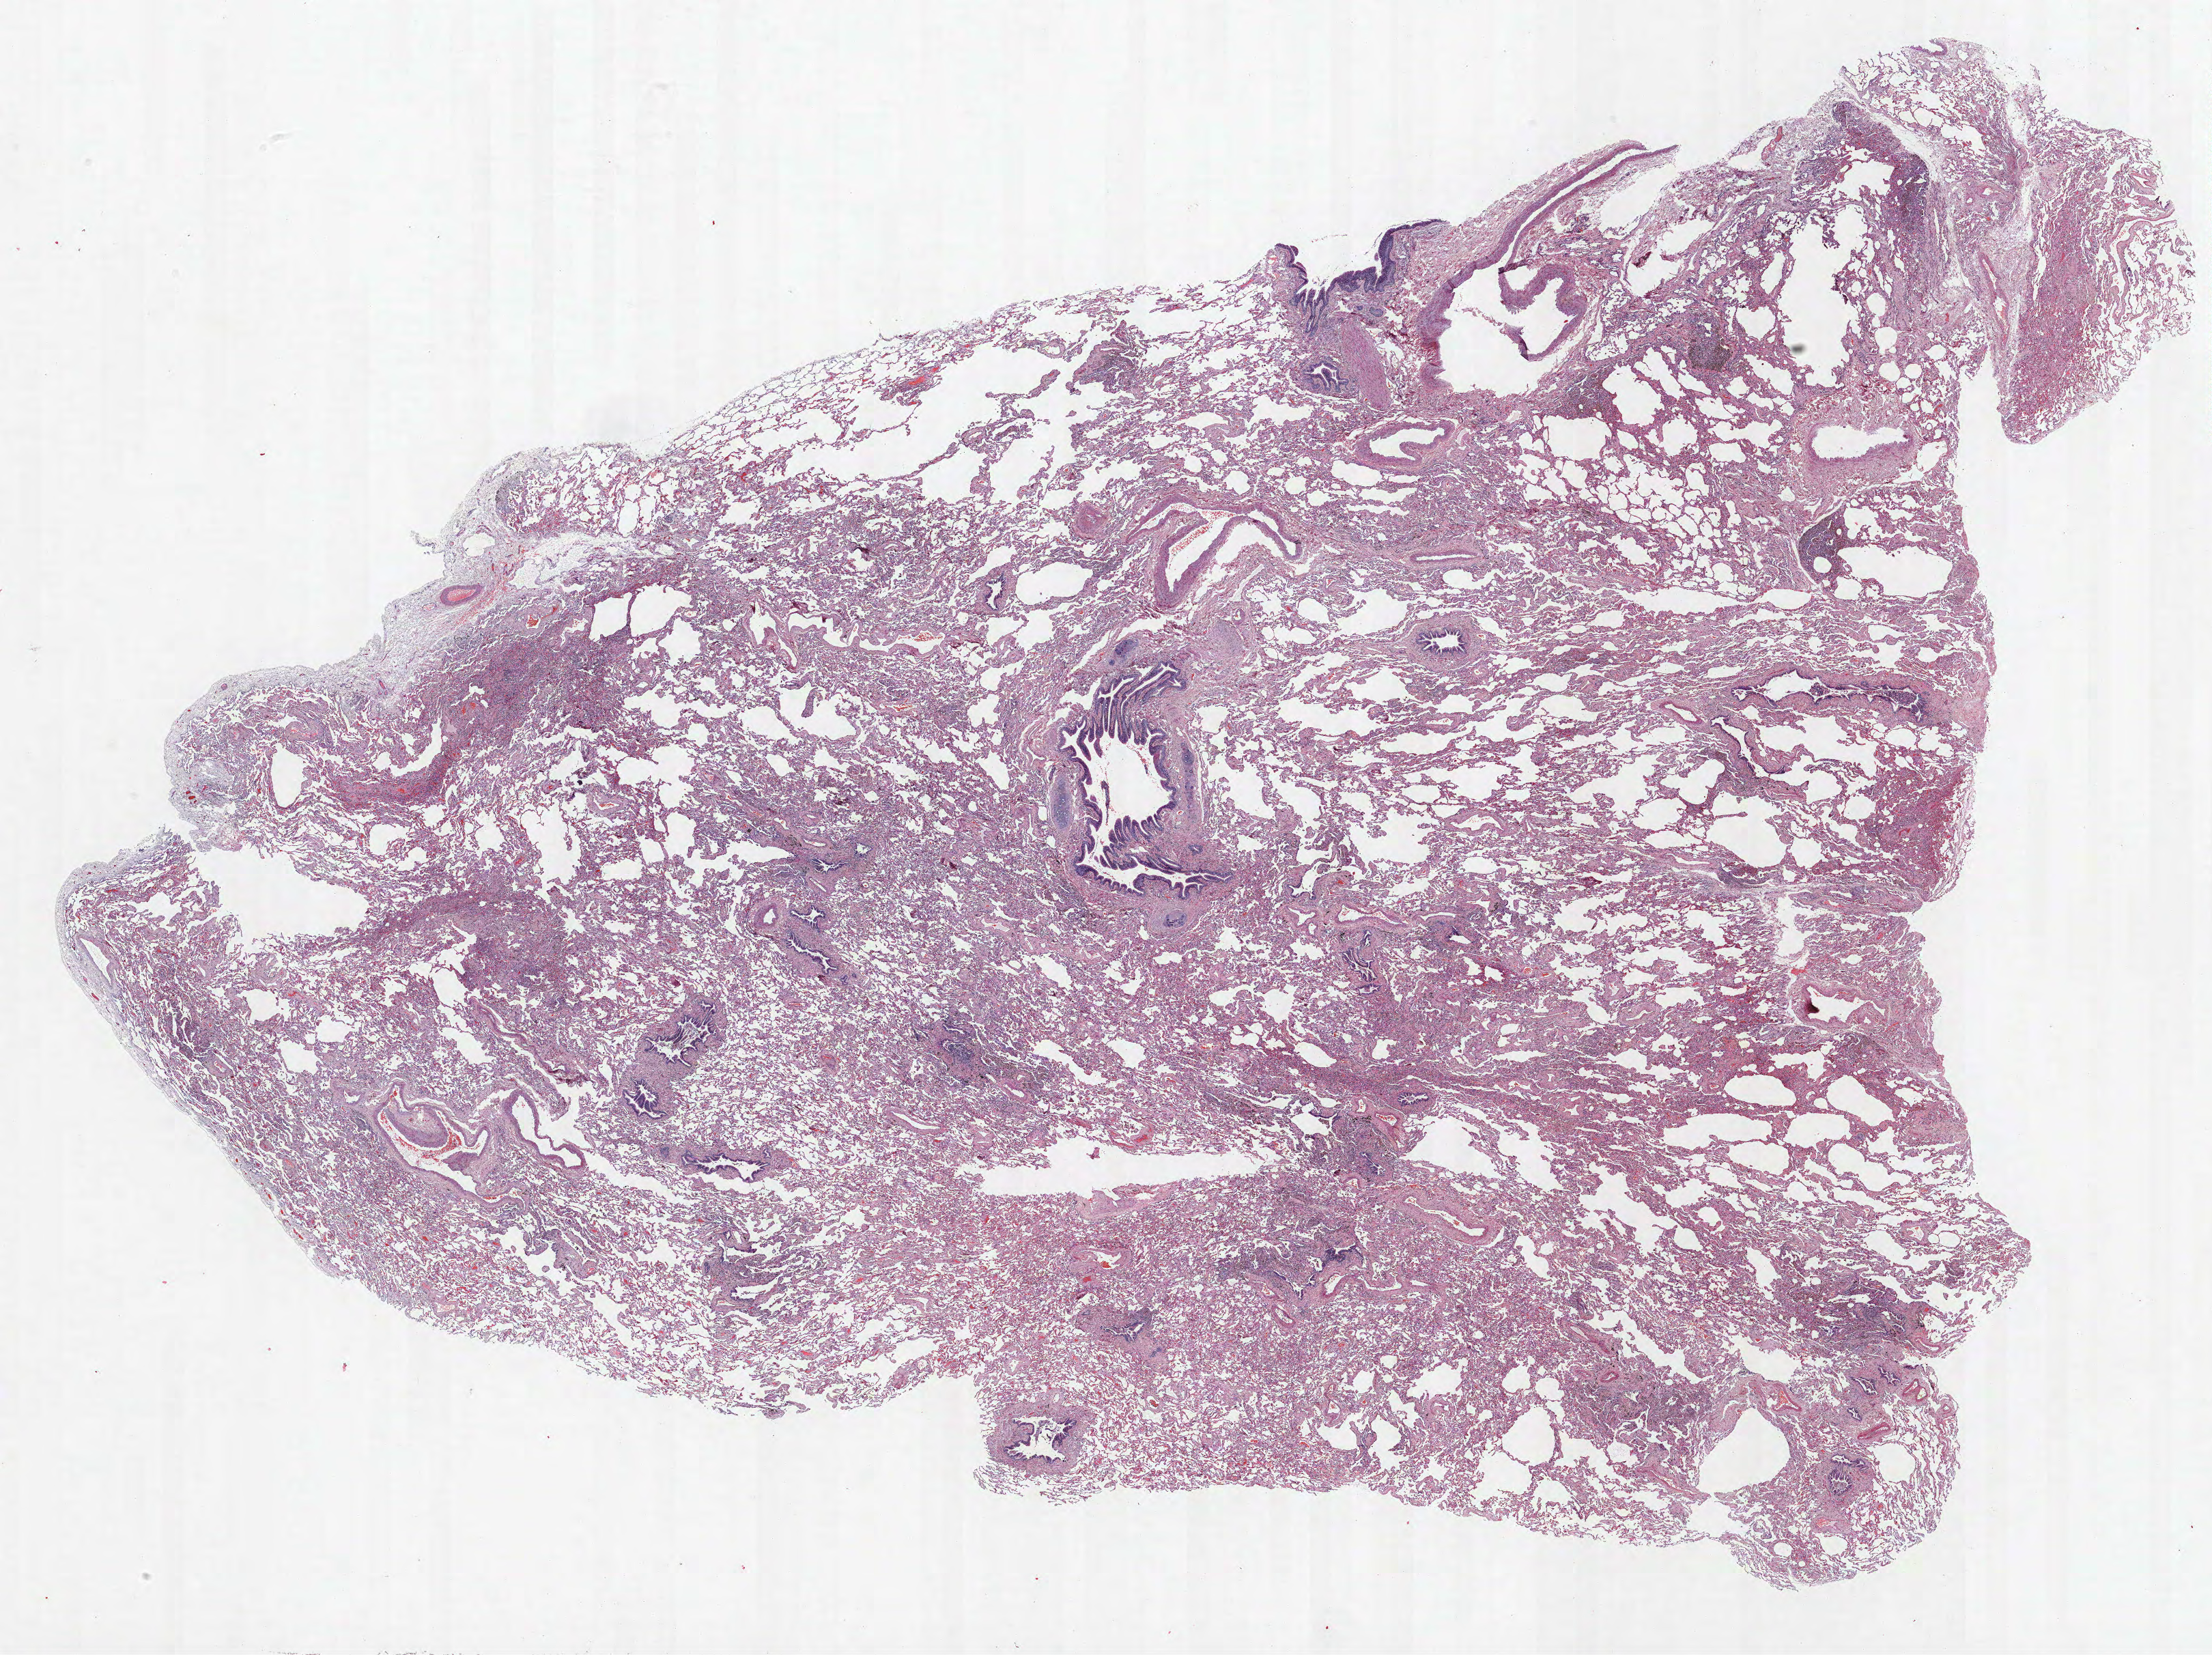
H&E-stained whole-slide image, shown as a low-resolution overview of the whole scanned area (about 25.9 x 19.4 mm, from a 40x scan), FFPE section, lung tissue. Male patient, aged 64 at enrolment. Current smoker at enrolment. Grade: moderately differentiated (G2).
Stage (AJCC 6th edition): IA. Primary tumour location (clinical record): right lower lobe. Participant's lung-cancer diagnosis: Adenocarcinoma, NOS. Tumour size (pathology): 28 mm.